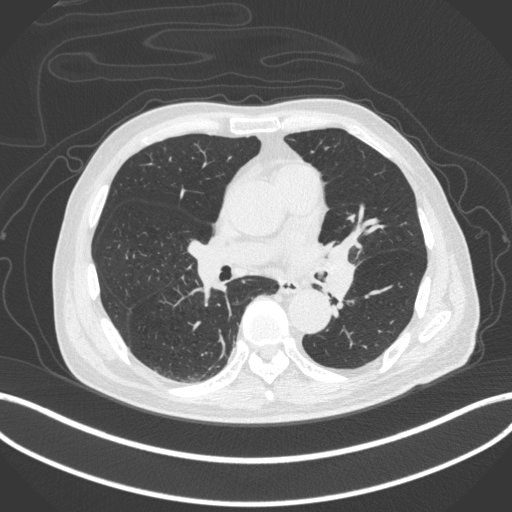
Chest CT, one axial slice. Slice 227 of 420 in the series (ordered by position). Lung window (W 1500 / L -600 HU). 1 mm slice thickness. 512 × 512 image matrix, field of view 400 × 400 mm. Patient: male, 77 years. From the clinical record (not read from this slice): clinical TNM (as recorded): T3 N1 M0.
Annotated regions visible in this slice (rectangle marked by the reading radiologist):
- lung tumour (recorded histology: adenocarcinoma): bounding box (x1, y1, x2, y2) in pixels: (319, 238, 360, 304)